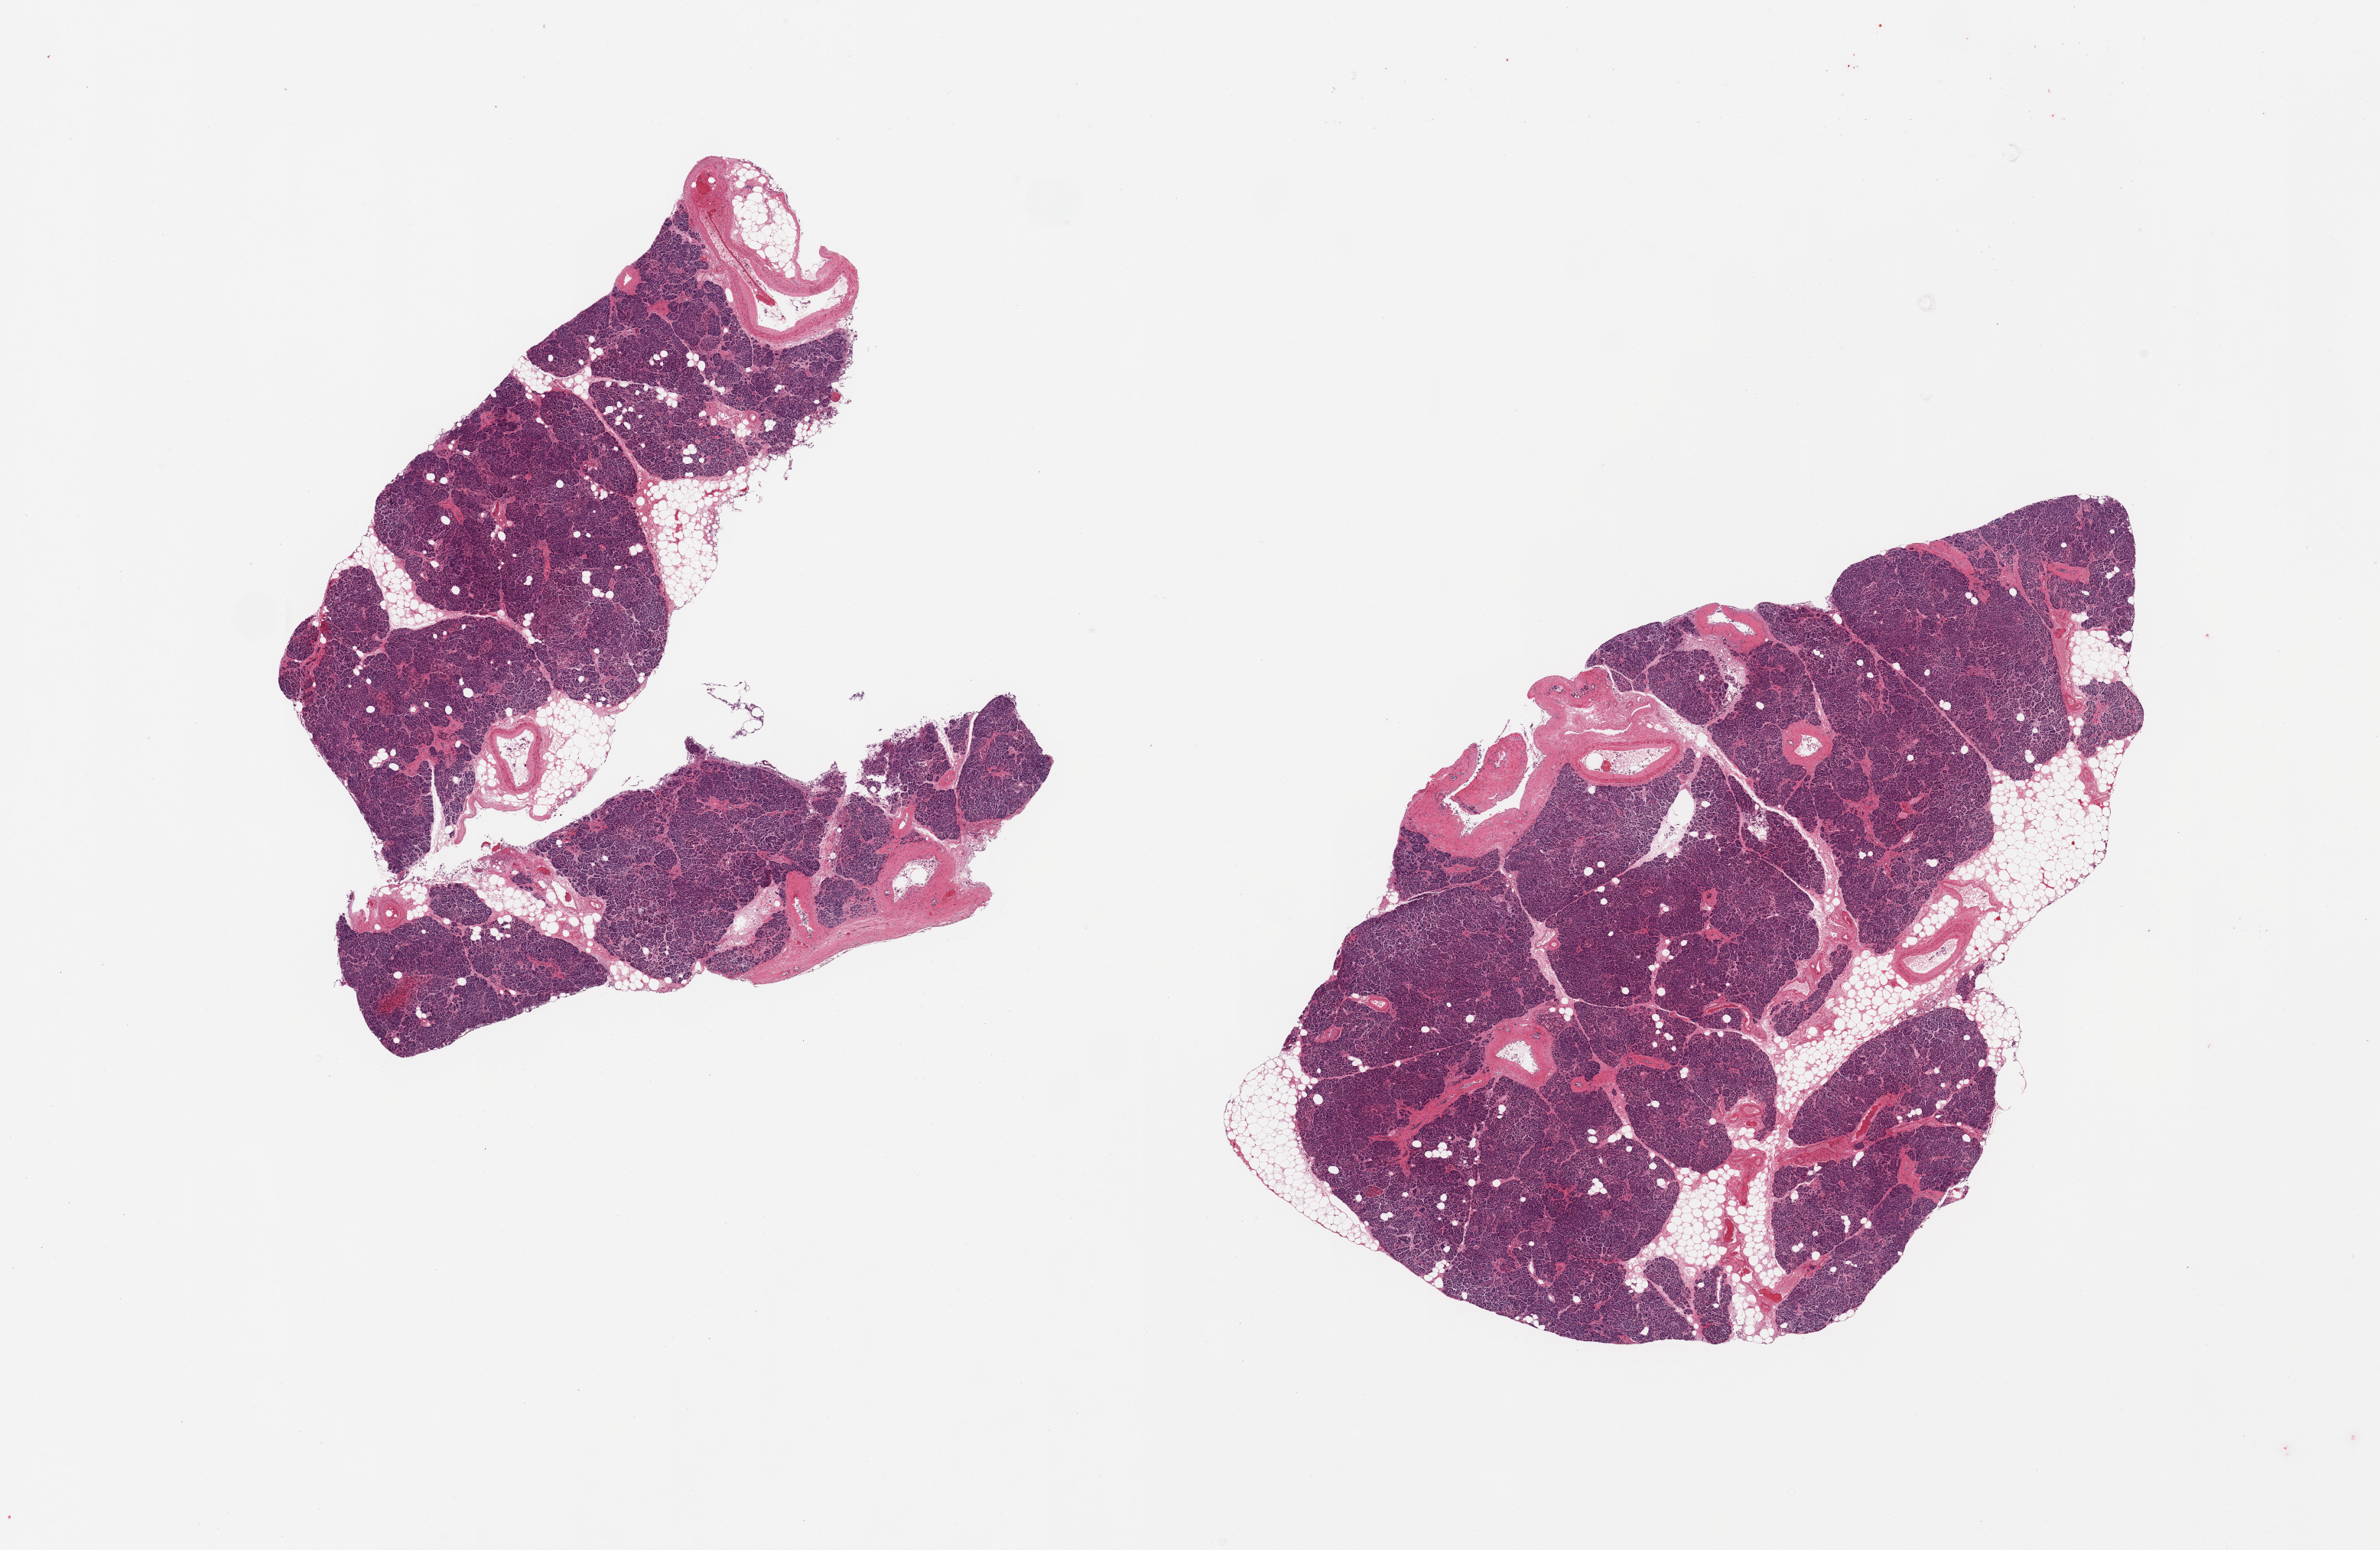
Whole-slide image, haematoxylin and eosin stain, shown as a low-resolution overview of the whole scanned area (about 24.6 x 16.0 mm). PAXgene-fixed paraffin-embedded (PFPE) section. Target tissue: pancreas. Donor tissue sample. Male donor.
Review note (as recorded): 2 pieces, ~10-20% fat; few Islets, well preserved.